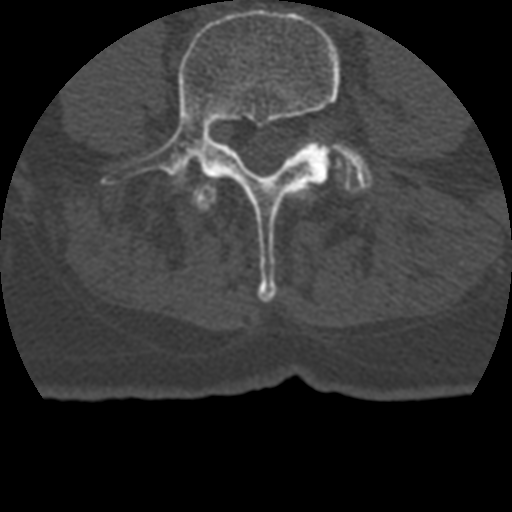
CT including the spine, one axial slice; slice 65 of 399 in the series (ordered by position); reconstruction kernel STANDARD; bone window (W 1800 / L 400 HU); 1.25 mm slice thickness; 512 × 512 image matrix. Patient age 69 years. Case-level facts recorded for this patient, not image findings: primary cancer: prostate.
Annotated regions visible in this slice (semi-automatically segmented with operator editing):
- L3 vertebra: bounding box <196,182,314,210> (left, top, right, bottom; pixels)
- L4 vertebra: <103,9,340,302>
- L5 vertebra: <330,145,372,193>